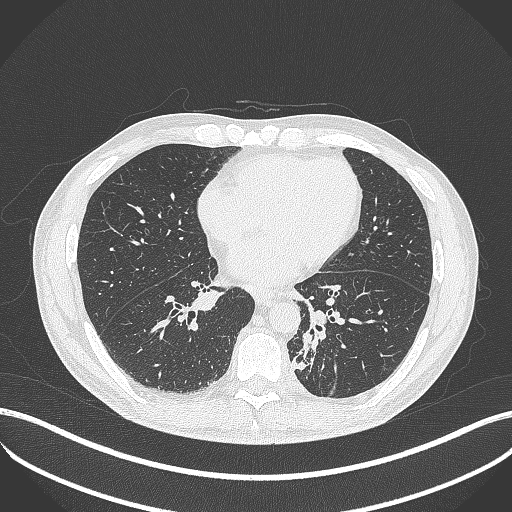
Chest CT, one axial slice; 120 kVp; lung window (W 1500 / L -600 HU); 1 mm slice thickness; 512 × 512 image matrix. Patient: male, 72 years. Case-level facts recorded for this patient, not image findings: clinical TNM (as recorded): T2b N0 M1.
Outlined on this slice (bounding box drawn by a radiologist):
- lung tumour (recorded histology: adenocarcinoma): bounding box <293,329,322,375> (left, top, right, bottom; pixels)